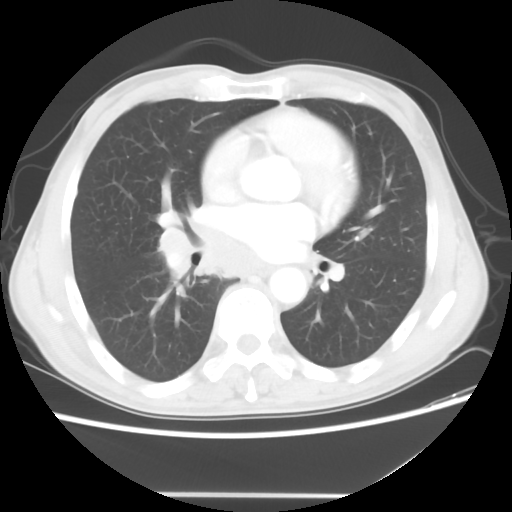
Chest CT, one axial slice; 120 kVp; lung window (W 1500 / L -600 HU); 512 × 512 image matrix, field of view 344 × 344 mm. Male patient, age 65 years. From the clinical record (not read from this slice): clinical TNM (as recorded): T1c N3 M0; histopathological grade: G3.
Structures marked on this image (bounding box drawn by a radiologist):
- lung tumour (recorded histology: small cell carcinoma): box from (x=160, y=220) to (x=269, y=285) px